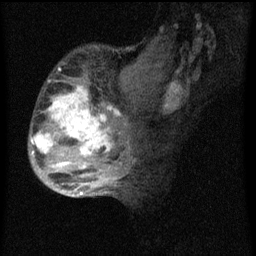
Breast MRI (dynamic contrast-enhanced), one sagittal slice; slice 25 of 60 in the series (ordered by position); dynamic contrast-enhanced series, image 2 of 4 at this slice position (ordered by acquisition); 1.5 T; TE 4.2 ms, TR 8 ms; 2 mm slice thickness; 256 × 256 image matrix, field of view 180 × 180 mm. Patient: female, 50 years.
Annotated regions visible in this slice (semi-automatically segmented with operator editing):
- analysis volume of interest (the breast-tissue region the enhancement analysis was run in; not a lesion): bounding box [x1, y1, x2, y2] px = [29, 46, 124, 177]
- tumour enhancement mask (voxels above the 70 % enhancement threshold inside the analysis volume of interest): [32, 86, 122, 169]